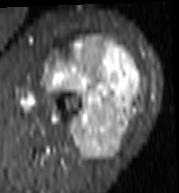
MRI of an extremity soft-tissue mass, one axial slice. Slice 61 of 103 in the series (ordered by position). STIR. MR volume resampled by the dataset authors to the PET/CT grid (not the native acquisition matrix). 179 × 193 image matrix, field of view 175 × 188 mm. Female patient. From the clinical record (not read from this slice): histological type: undifferentiated – high grade; grade: high; site of the primary tumour: left thigh.
Annotated regions visible in this slice (expert contour drawn on MRI and transferred to this co-registered scan by the dataset authors):
- gross tumour volume including surrounding oedema: box from (x=43, y=37) to (x=142, y=161) px
- gross tumour volume (mass): (x=43, y=37)–(x=142, y=161)